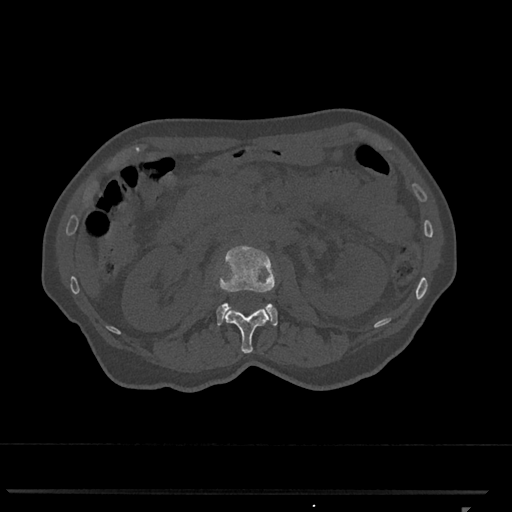
CT including the spine, one axial slice; slice 374 of 793 in the series (ordered by position); bone window (W 1800 / L 400 HU); 0.5 mm slice thickness; 512 × 512 image matrix. Patient: female, 62 years. From the clinical record (not read from this slice): primary cancer: renal.
Outlined on this slice (semi-automatically segmented with operator editing):
- L1 vertebra: bounding box (x1, y1, x2, y2) in pixels: (225, 308, 270, 354)
- L2 vertebra: (217, 245, 278, 326)